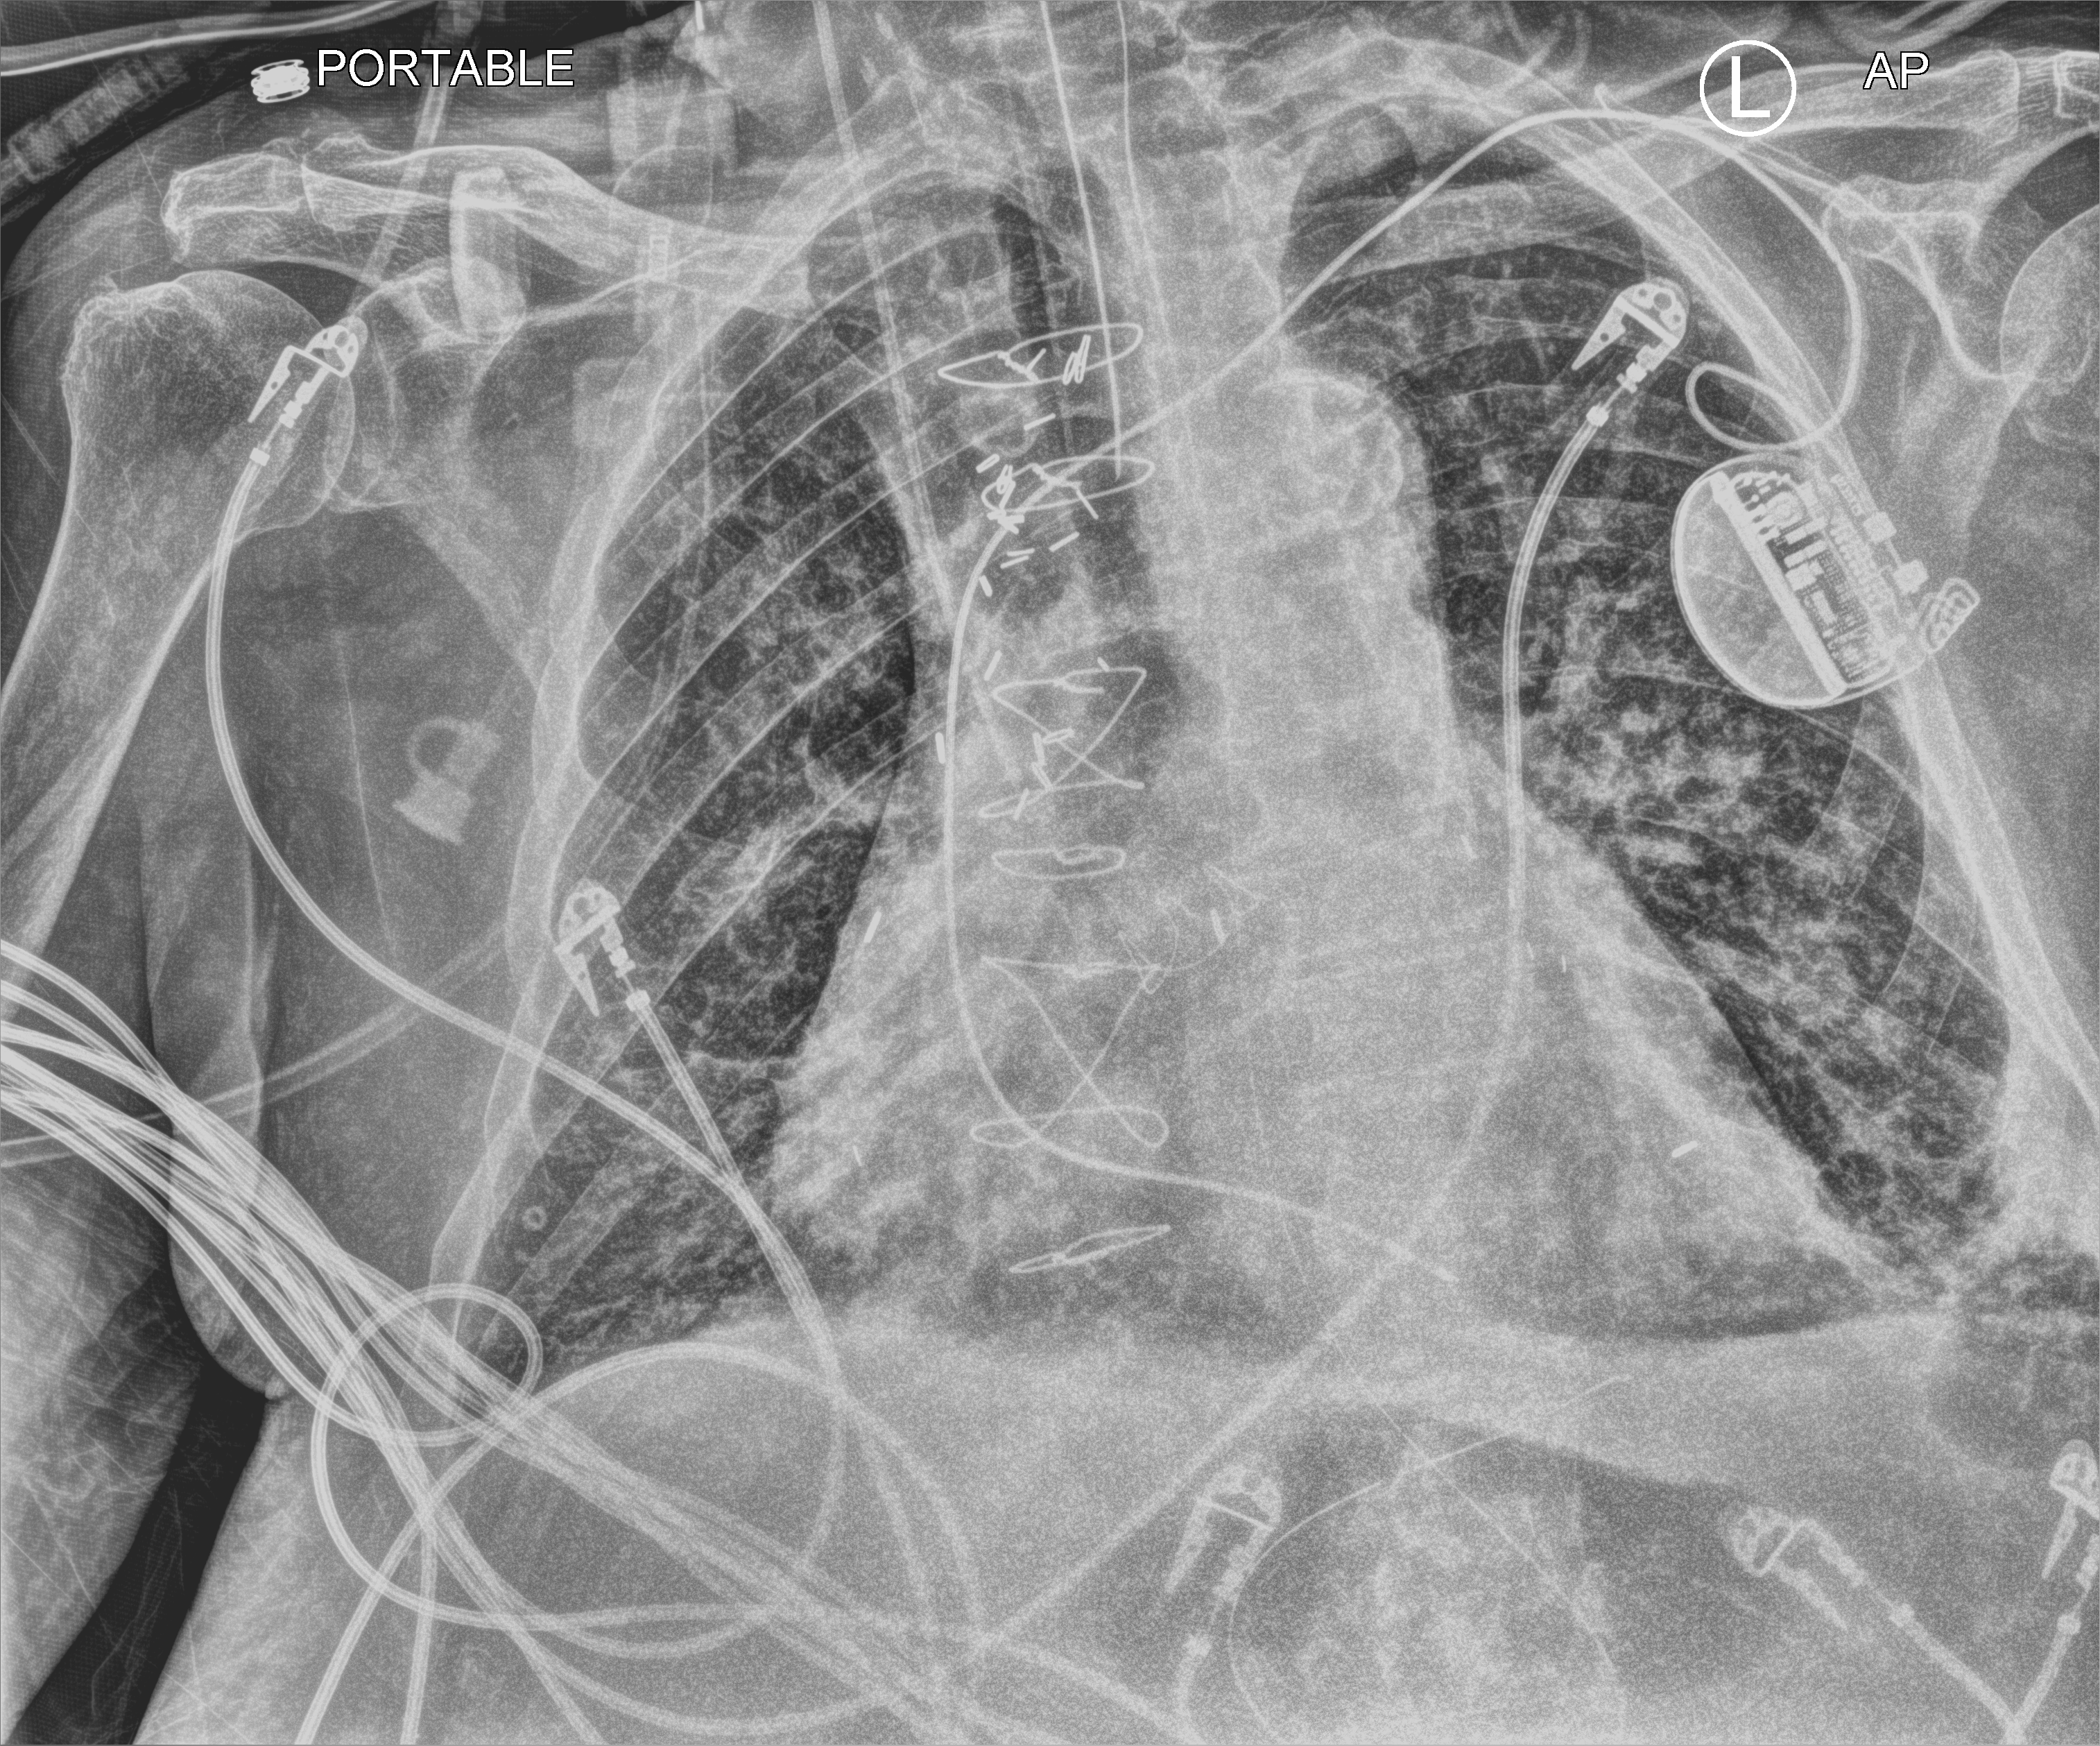
Bedside chest radiograph (computed radiography); anteroposterior (AP) projection. Male patient hospitalised with COVID-19, age 75–90 years.
Admission-level facts for this patient (not findings on this image; timing relative to this image not recorded):
- mechanically ventilated during this hospital stay: yes
- admitted to intensive care during this hospital stay: yes